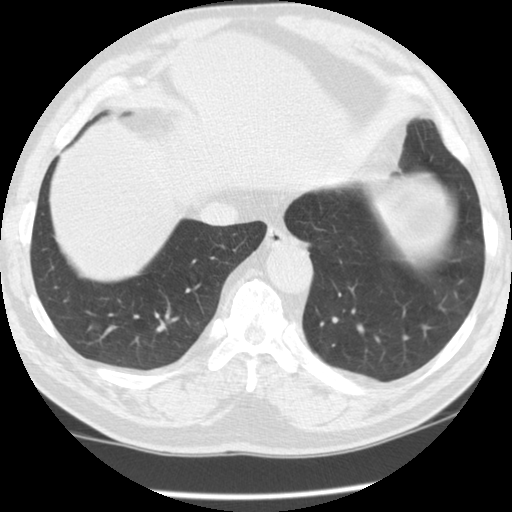
Low-dose screening chest CT, one axial slice. Slice 26 of 115 in the series (ordered by position). Reconstruction kernel STANDARD. 120 kVp. Lung window (W 1500 / L -600 HU). 512 × 512 image matrix, field of view 330 × 330 mm.
Annotated regions visible in this slice (outlined manually by an expert reader):
- lesion 1 (tumor, lower lobe of right lung): box from (x=88, y=326) to (x=92, y=330) px